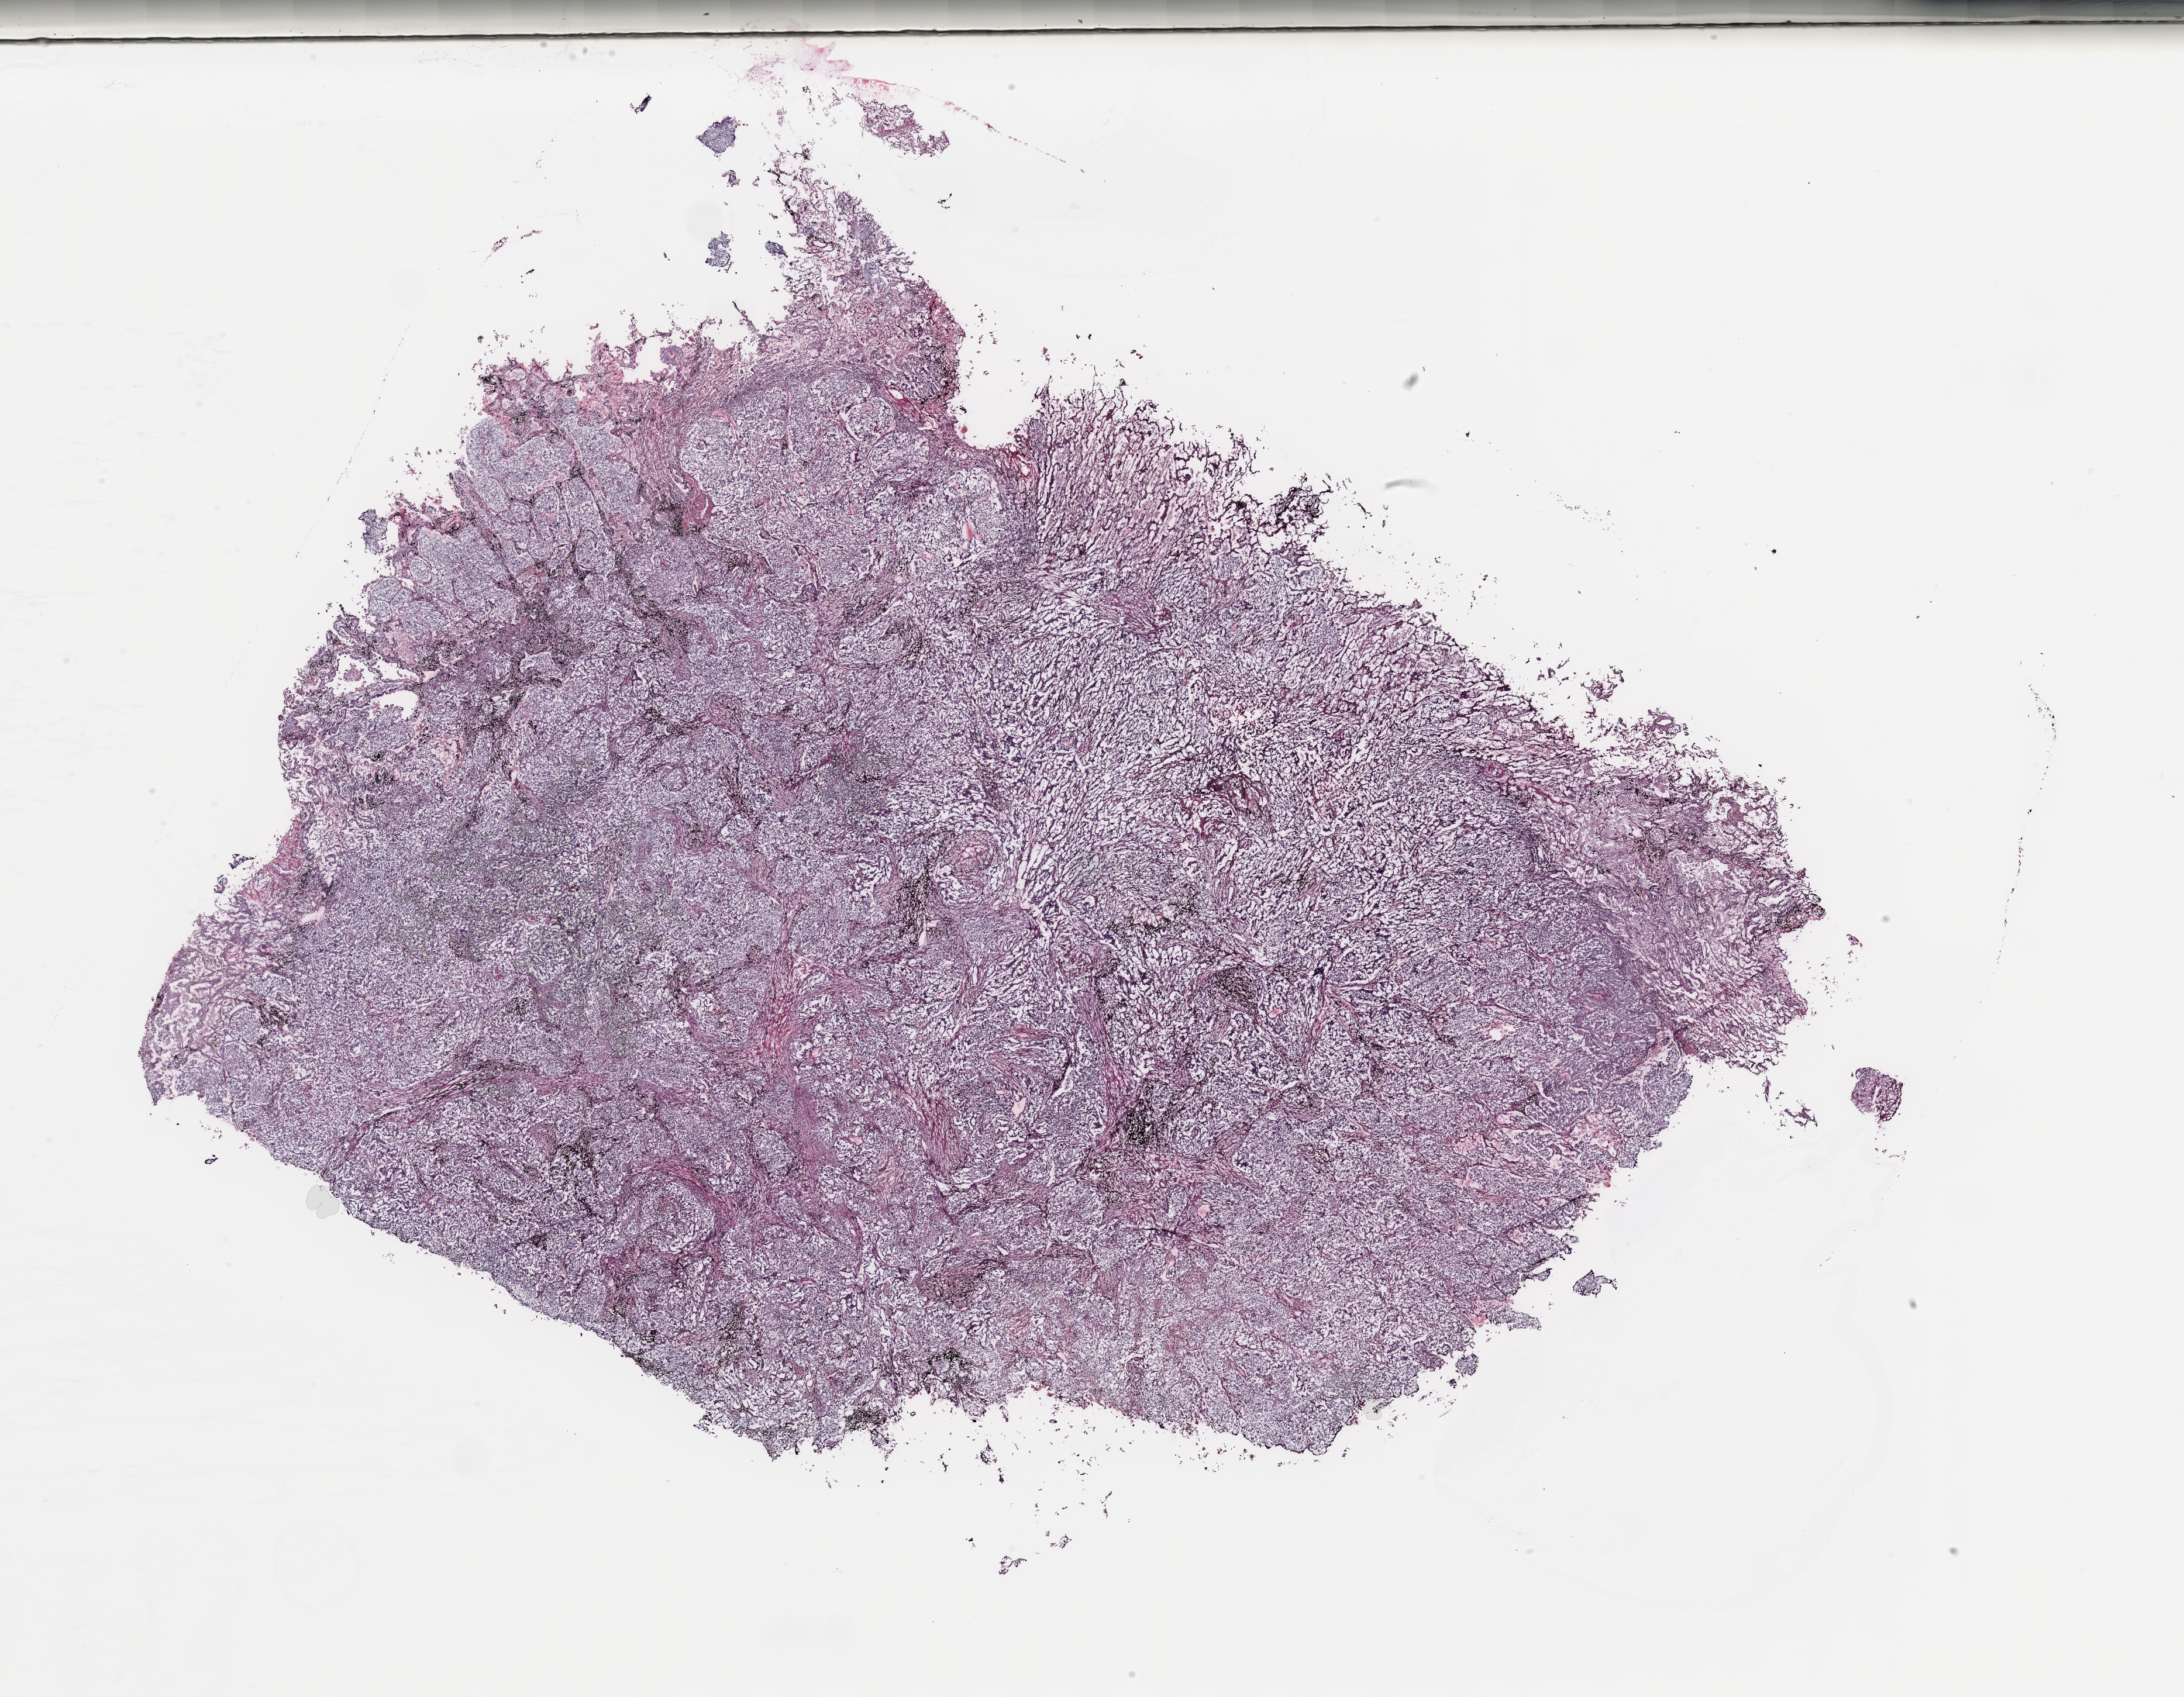
Whole-slide histology image, Hematoxylin and eosin (H&E) stained — low-resolution overview of the scanned area, about 29.5 x 23.0 mm, tumour tissue sample, sampled site: lung. Male, 53 y/o. Histologic grade: GX (grade cannot be assessed). Pathologist review of this section (percent, as recorded): tumour nuclei 75%, necrosis 5%.
AJCC pathologic stage: IB. Diagnosis: Adenocarcinoma, NOS.